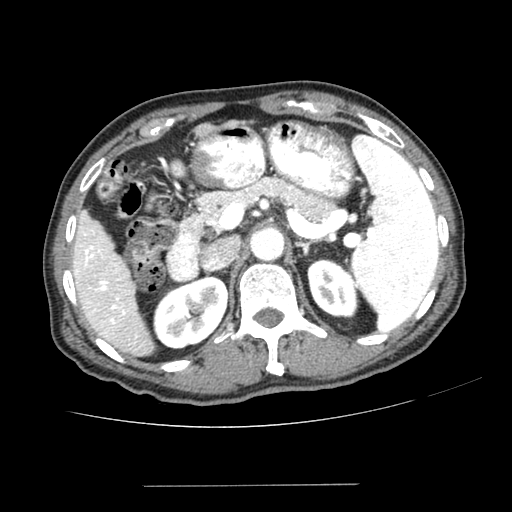
Contrast-enhanced abdominal CT (liver protocol), one axial slice. Slice 146 of 187 in the series (ordered by position). 100 kVp. One of 2 acquisitions stored at this slice position. Soft-tissue window (W 400 / L 40 HU). 2.5 mm slice thickness. 512 × 512 image matrix, field of view 360 × 360 mm. From the clinical record (not read from this slice): diagnosis: hepatocellular carcinoma (patient treated with transarterial chemoembolisation; whether this scan precedes or follows treatment is not stated here); TNM stage (as recorded): Stage-I; Child-Pugh class: A; tumour differentiation: poorly differentiated; tumour size: 1.6 cm.
Structures marked on this image (semi-automatically segmented with operator editing):
- liver parenchyma outside the tumour (the mass and vessels are separate outlines, so this box may not span the whole liver): bounding box <72,210,154,354> (left, top, right, bottom; pixels)
- liver vessels: <75,232,126,324>